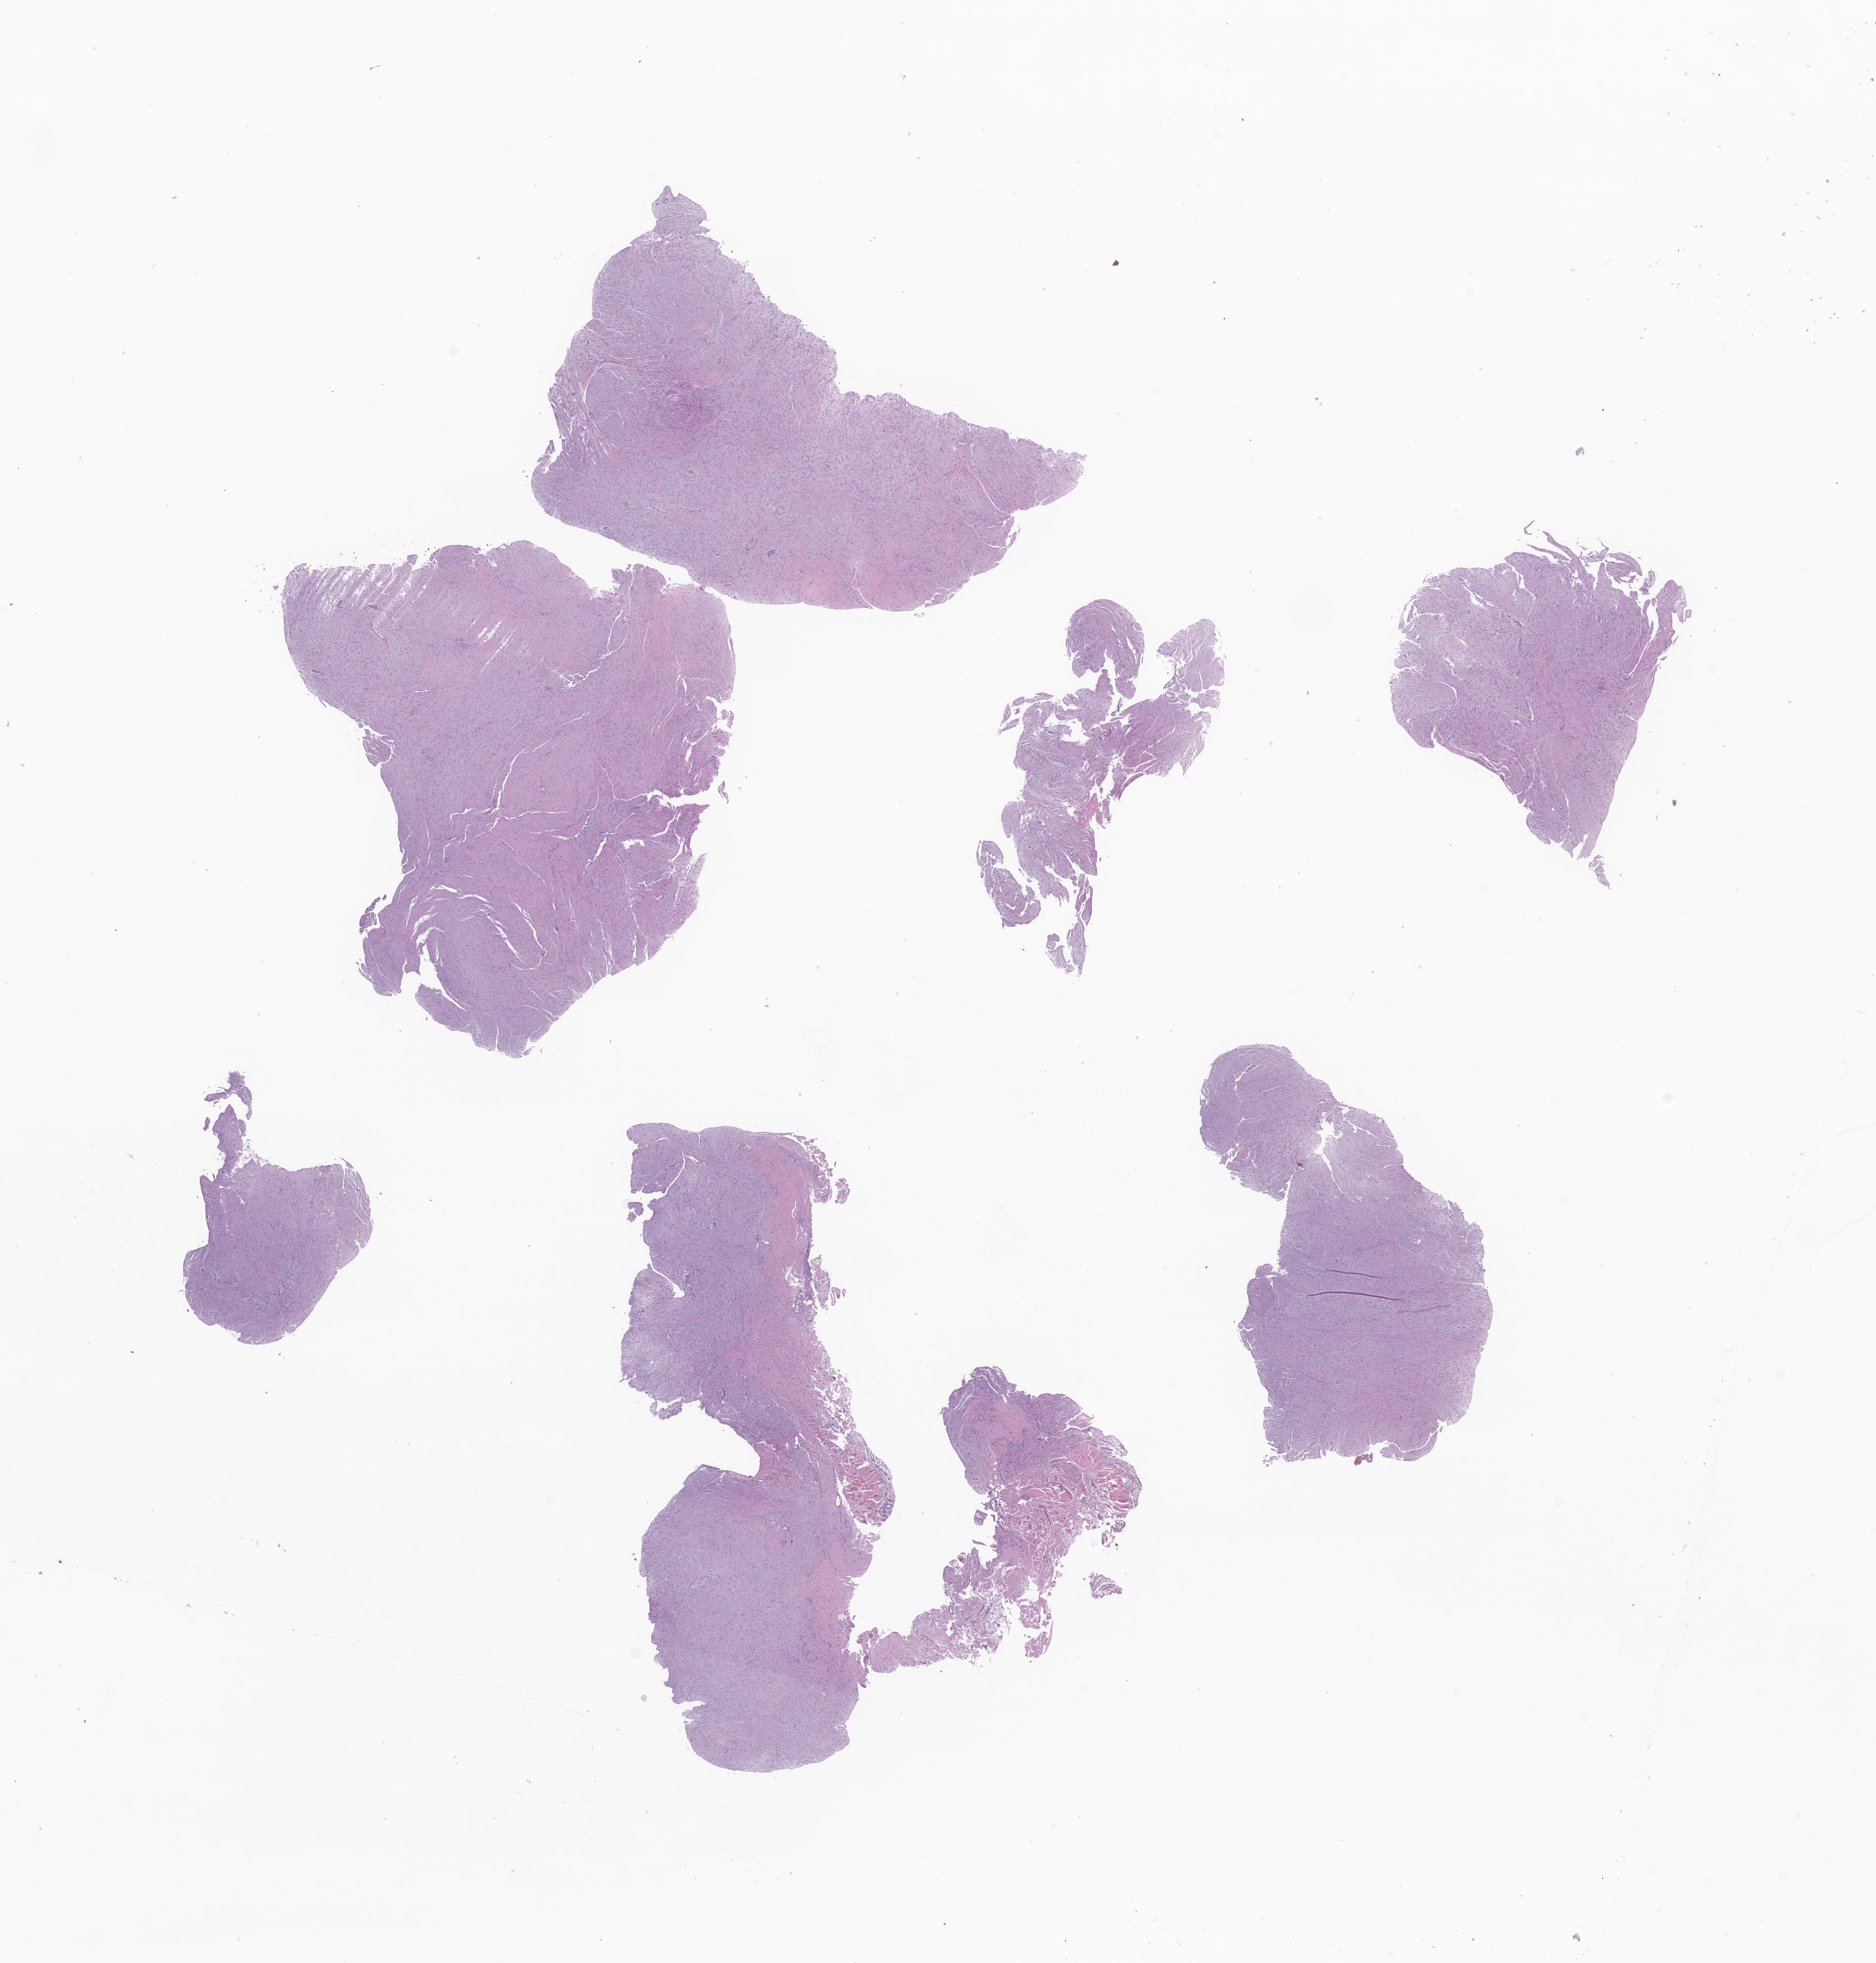
H&E whole-slide image of tumor tissue from the buccal mucosa, whole scanned area (about 18.7 x 19.6 mm) shown as a low-resolution overview; formalin-fixed paraffin-embedded section. Female patient, age 639 days.
• diagnosis (ICD-O-3 morphology term): Sclerotic fibroma